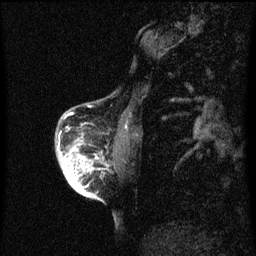
Breast MRI (dynamic contrast-enhanced), one sagittal slice. Slice 16 of 60 in the series (ordered by position). Dynamic contrast-enhanced series, image 2 of 3 at this slice position (ordered by acquisition). 1.5 T. TE 4.2 ms, TR 8 ms. 2 mm slice thickness. 256 × 256 image matrix, field of view 180 × 180 mm. Female patient, age 56 years.
Annotated regions visible in this slice (semi-automatic segmentation, software-assisted and operator-edited):
- analysis volume of interest (the breast-tissue region the enhancement analysis was run in; not a lesion): bounding box [x1, y1, x2, y2] px = [56, 122, 111, 199]
- tumour enhancement mask (voxels above the 70 % enhancement threshold inside the analysis volume of interest): [57, 146, 99, 199]